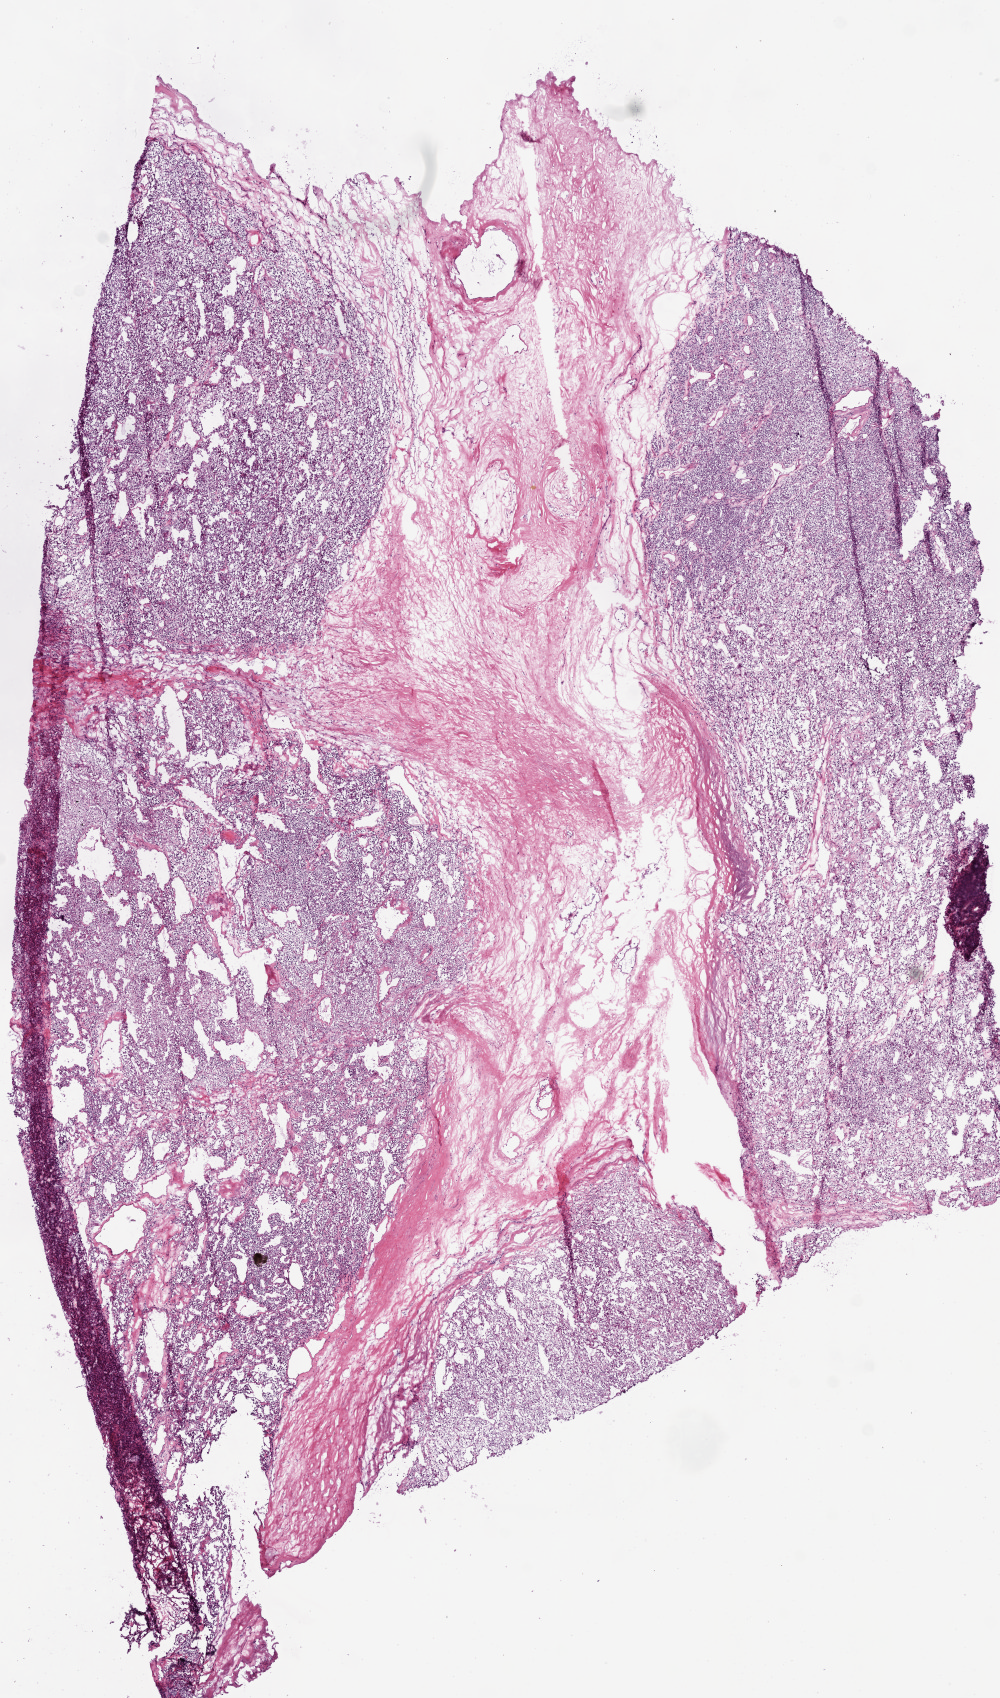
Digitized H&E-stained tissue section (whole slide) — a low-resolution overview of the entire scanned area, about 8.0 x 13.6 mm (acquisition: 20x scan). Frozen section from the bottom of the tissue portion. Primary tumour sample from the kidney. Female patient; age at initial diagnosis 76 years. Histologic grade: G2 (moderately differentiated). Slide review estimates, as recorded: tumour cells 70%, tumour nuclei 85%, normal cells 0%, stromal cells 30%, necrosis 0%.
AJCC pathologic stage: III. Pathologic diagnosis: Clear cell adenocarcinoma, NOS.